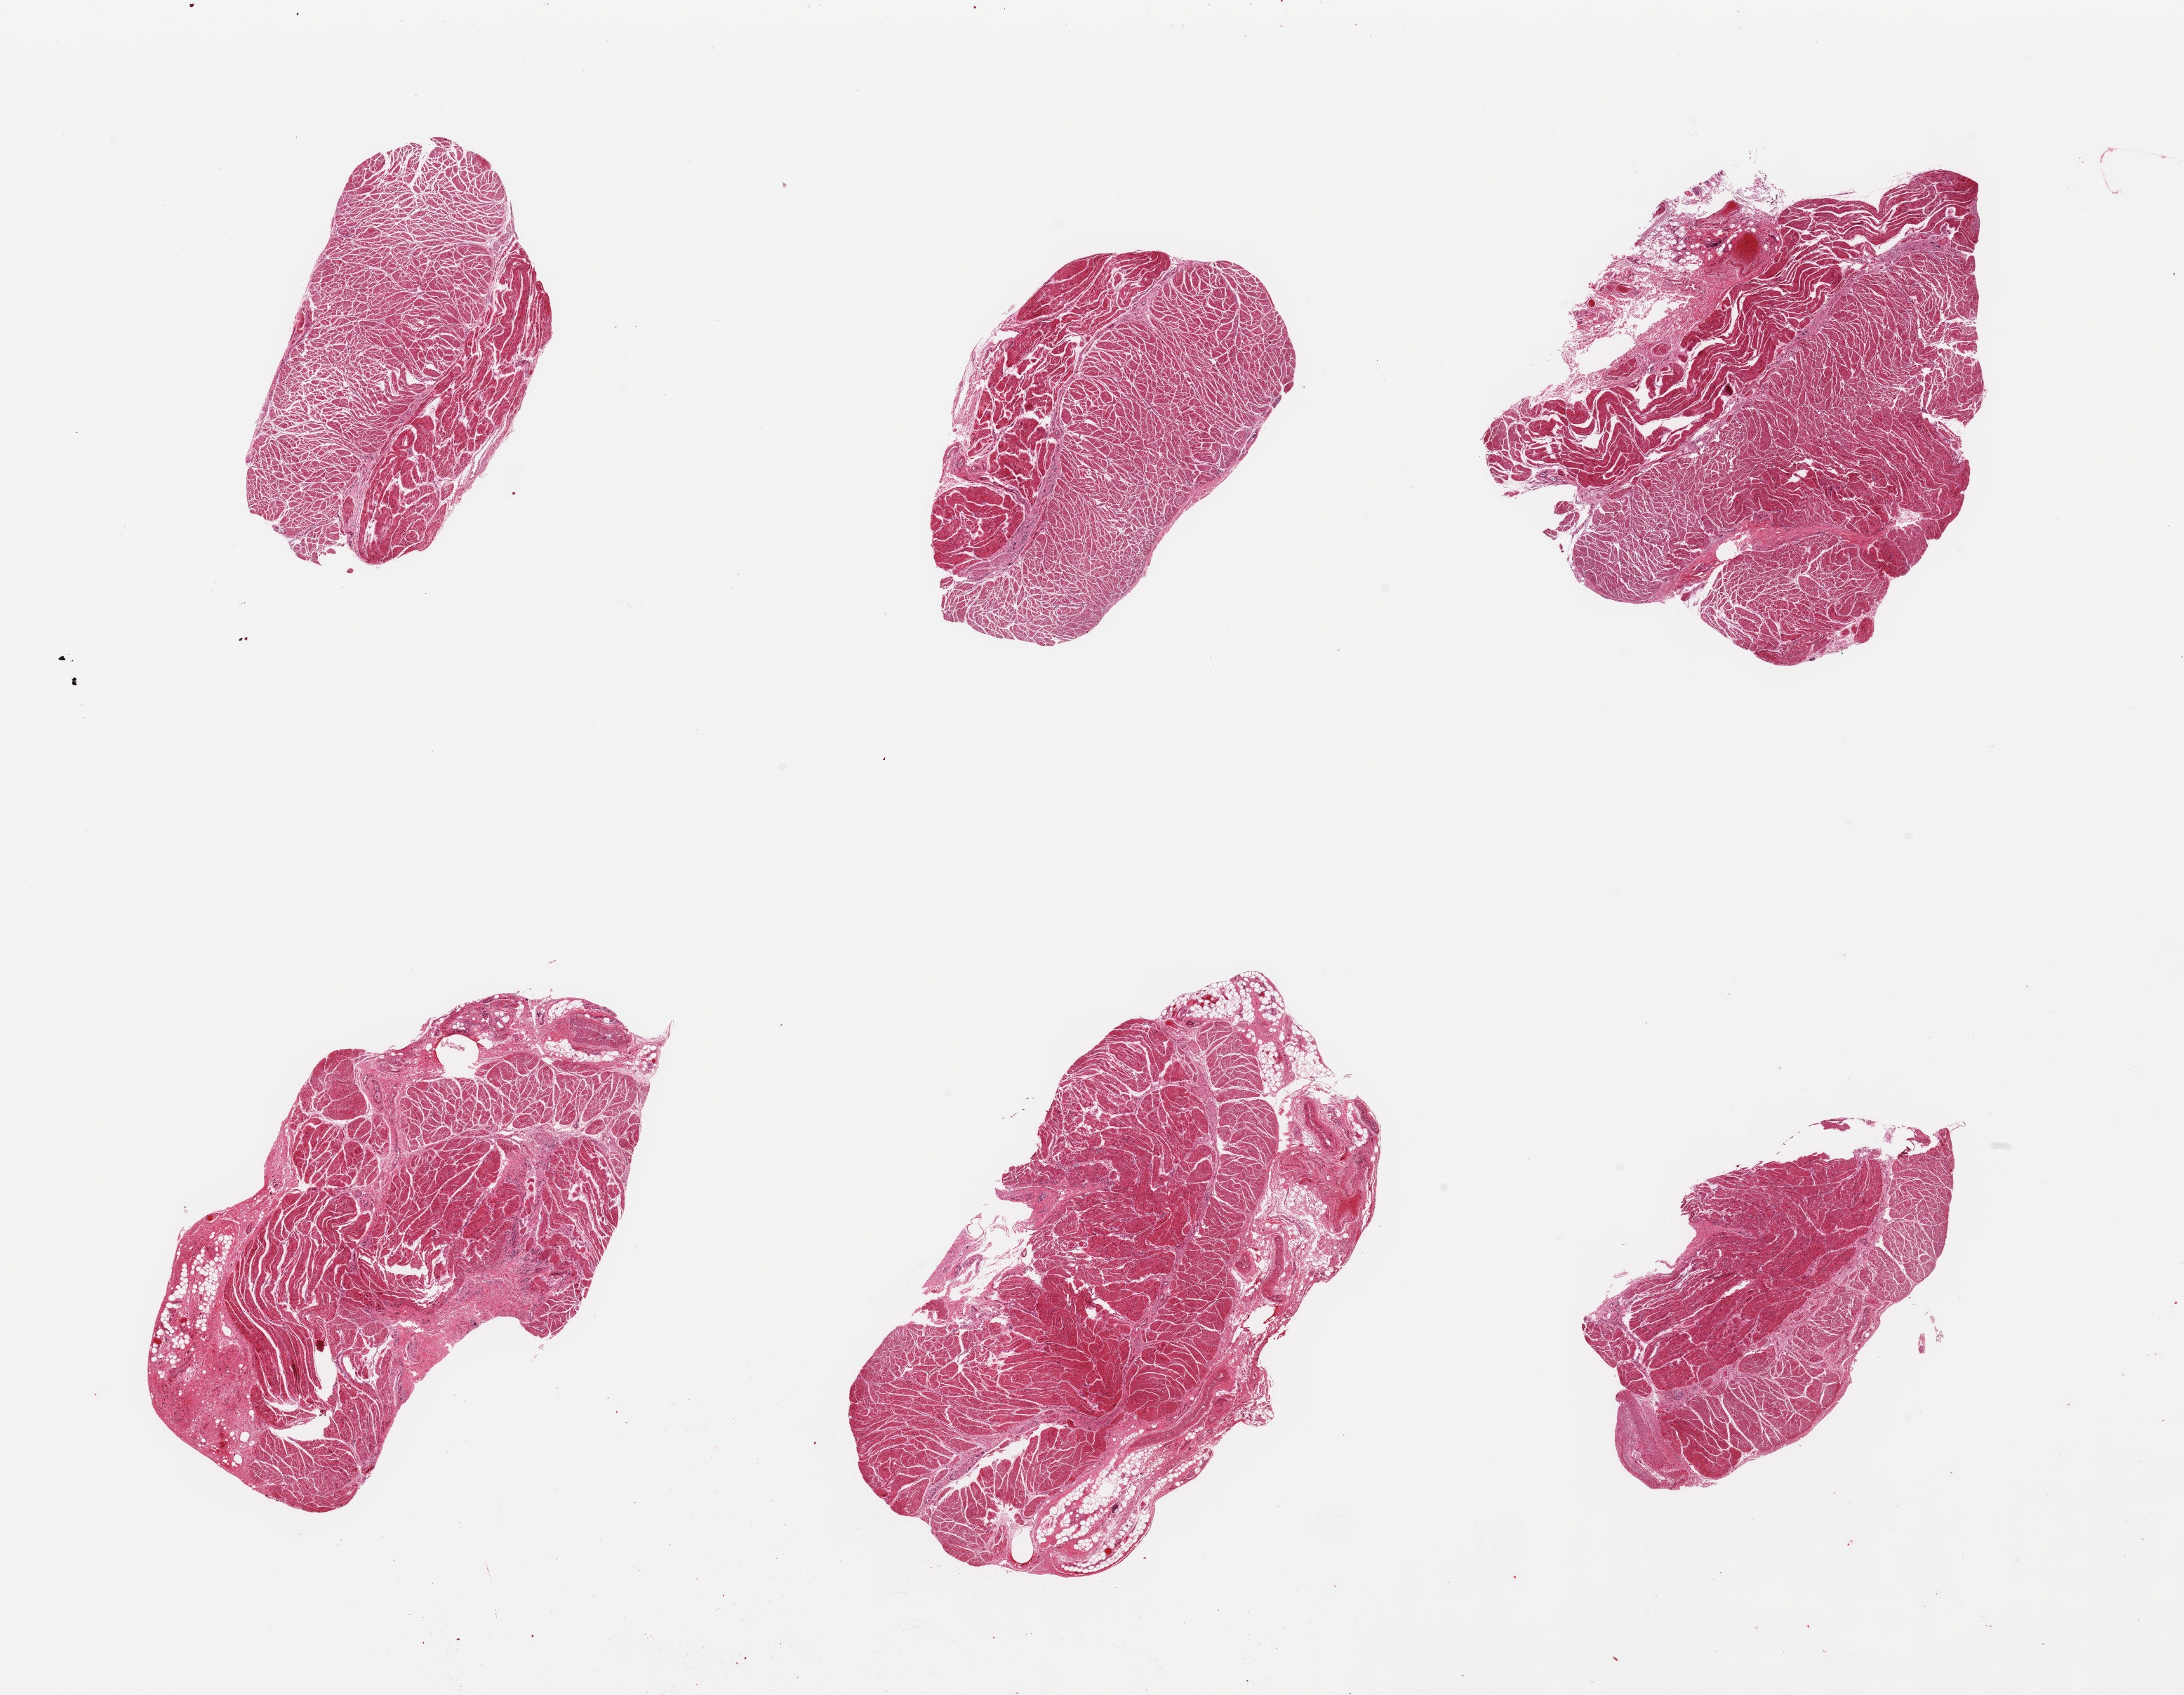
Whole-slide image, haematoxylin and eosin stain, low-resolution overview of the scanned area, about 24.6 x 19.1 mm; PAXgene-fixed paraffin-embedded (PFPE) section; section of esophageal muscle (target tissue); donor tissue sample. Donor sex: male.
Review note (as recorded): 6 pieces; target muscularis.